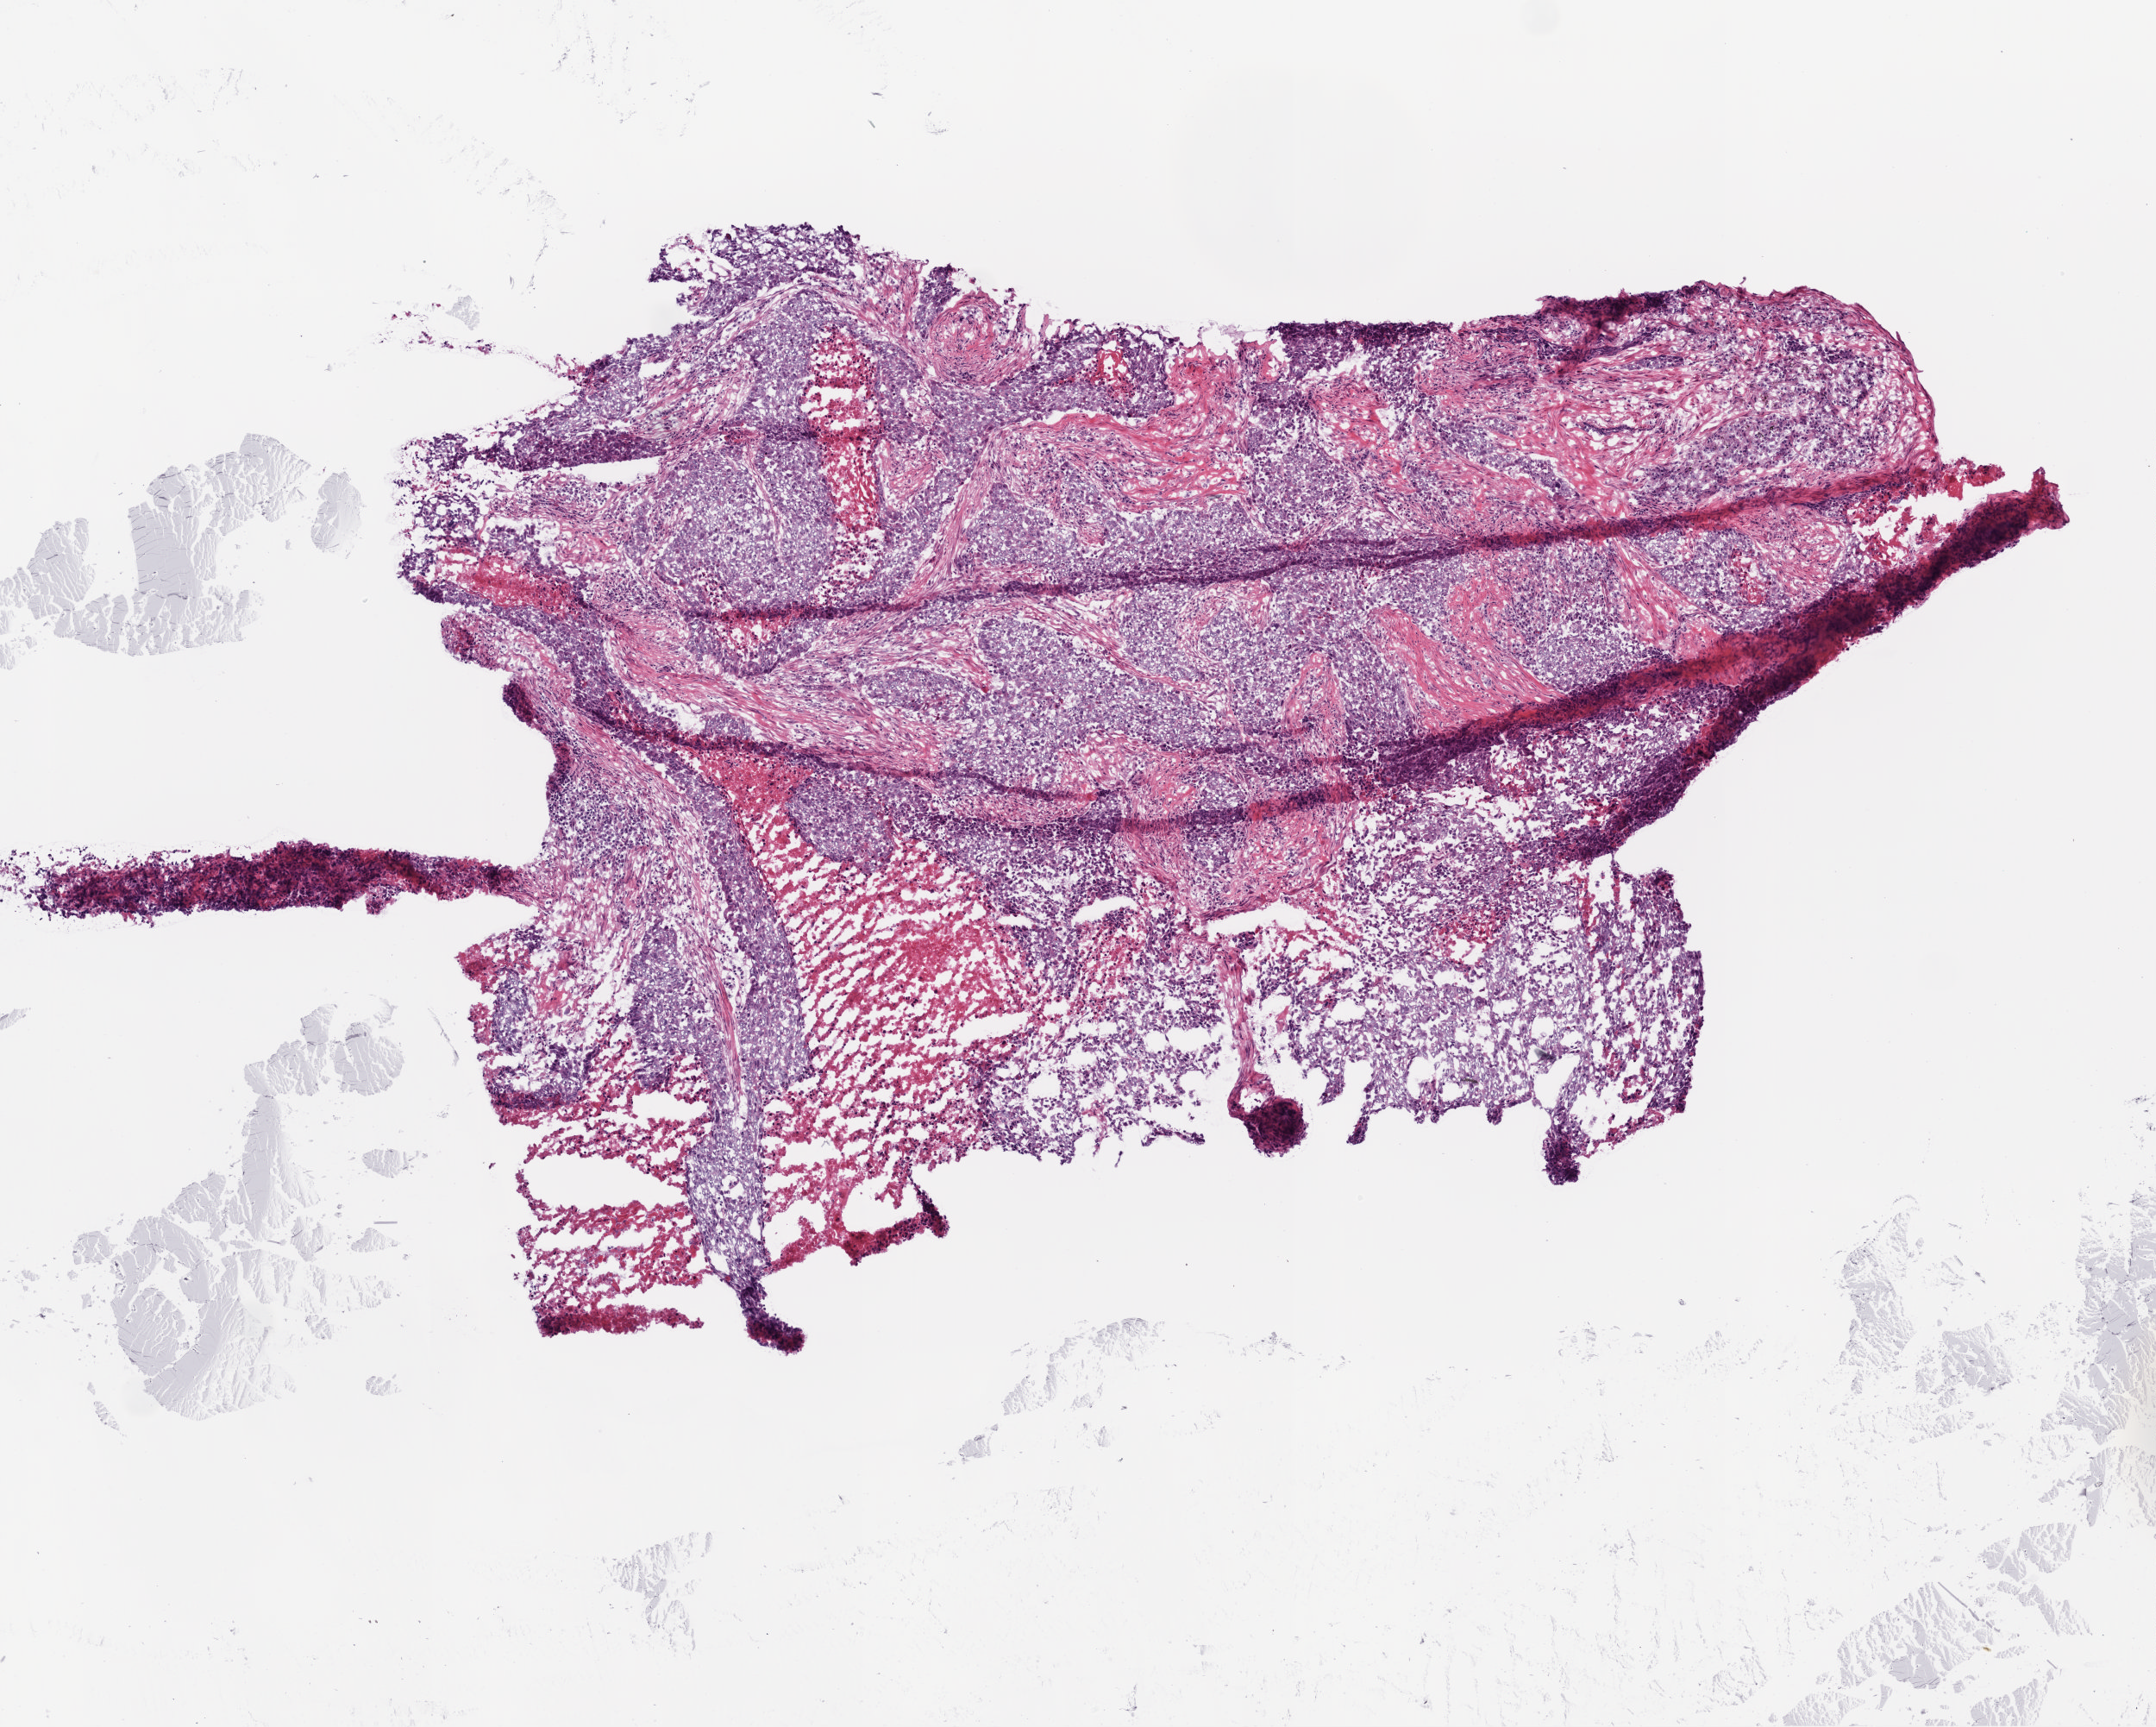
H&E whole-slide image — a low-resolution overview of the entire scanned area, about 5.0 x 4.0 mm, frozen section from the top of the tissue portion, lung, primary tumour sample. Patient: male, age at initial diagnosis 63 years. Composition of this section per pathologist review: tumour cells 70%, tumour nuclei 80%, normal cells 0%, stromal cells 15%, necrosis 10%.
• pathologic diagnosis: Squamous cell carcinoma, NOS (lower lobe, lung)
• AJCC pathologic stage: IIB
• laterality: left